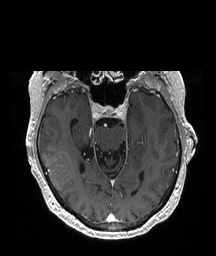
Brain MRI from a brain-tumour surgery series, one axial slice; position 132 of 208 along the scan axis; T1-weighted post-contrast; 1 mm slice thickness; 216 × 256 image matrix, field of view 216 × 256 mm. Case-level facts recorded for this patient, not image findings: histopathology: Glioblastoma; WHO grade: 4; IDH mutation: no; tumour location: Right Temporal.
Annotated regions visible in this slice (manually delineated by an expert):
- tumour: bounding box <44,151,74,191> (left, top, right, bottom; pixels)